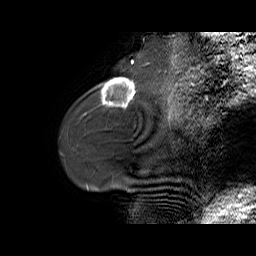
Breast MRI (dynamic contrast-enhanced), one sagittal slice. Slice 15 of 70 in the series (ordered by position). Dynamic contrast-enhanced series, time point 2 of 6 at this slice position (early post-contrast). 1.5 T. TE 5.5 ms, TR 32.9 ms. 4 mm slice thickness. 256 × 256 image matrix, field of view 240 × 240 mm. Female patient. From the clinical record (not read from this slice): setting: breast cancer imaged before/during neoadjuvant chemotherapy; receptor status: HER2-positive.
Annotated regions visible in this slice (semi-automatically segmented with operator editing):
- analysis volume of interest (the breast-tissue region the enhancement analysis was run in; not a lesion): box from (x=96, y=73) to (x=141, y=107) px
- tumour enhancement mask (voxels above the 100 % enhancement threshold inside the analysis volume of interest): (x=101, y=78)–(x=135, y=107)